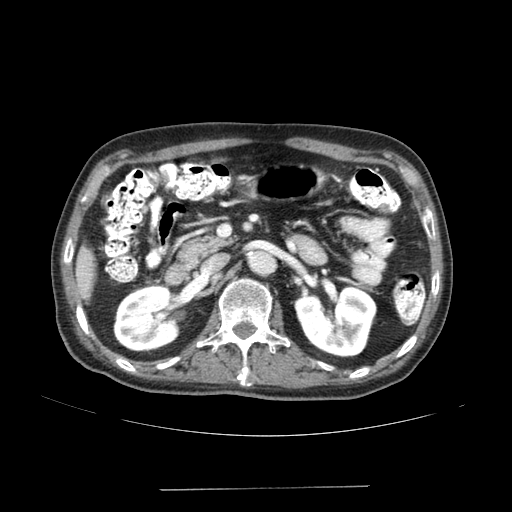
Contrast-enhanced abdominal CT (liver protocol), one axial slice; slice 60 of 192 in the series (ordered by position); reconstruction kernel SOFT; soft-tissue window (W 400 / L 40 HU); 512 × 512 image matrix, field of view 400 × 400 mm. Case-level facts recorded for this patient, not image findings: diagnosis: hepatocellular carcinoma (patient treated with transarterial chemoembolisation; whether this scan precedes or follows treatment is not stated here); TNM stage (as recorded): Stage-IVA; Child-Pugh class: A.
Structures marked on this image (semi-automatic segmentation, software-assisted and operator-edited):
- liver parenchyma outside the tumour (the mass and vessels are separate outlines, so this box may not span the whole liver): bounding box [x1, y1, x2, y2] px = [76, 246, 94, 300]